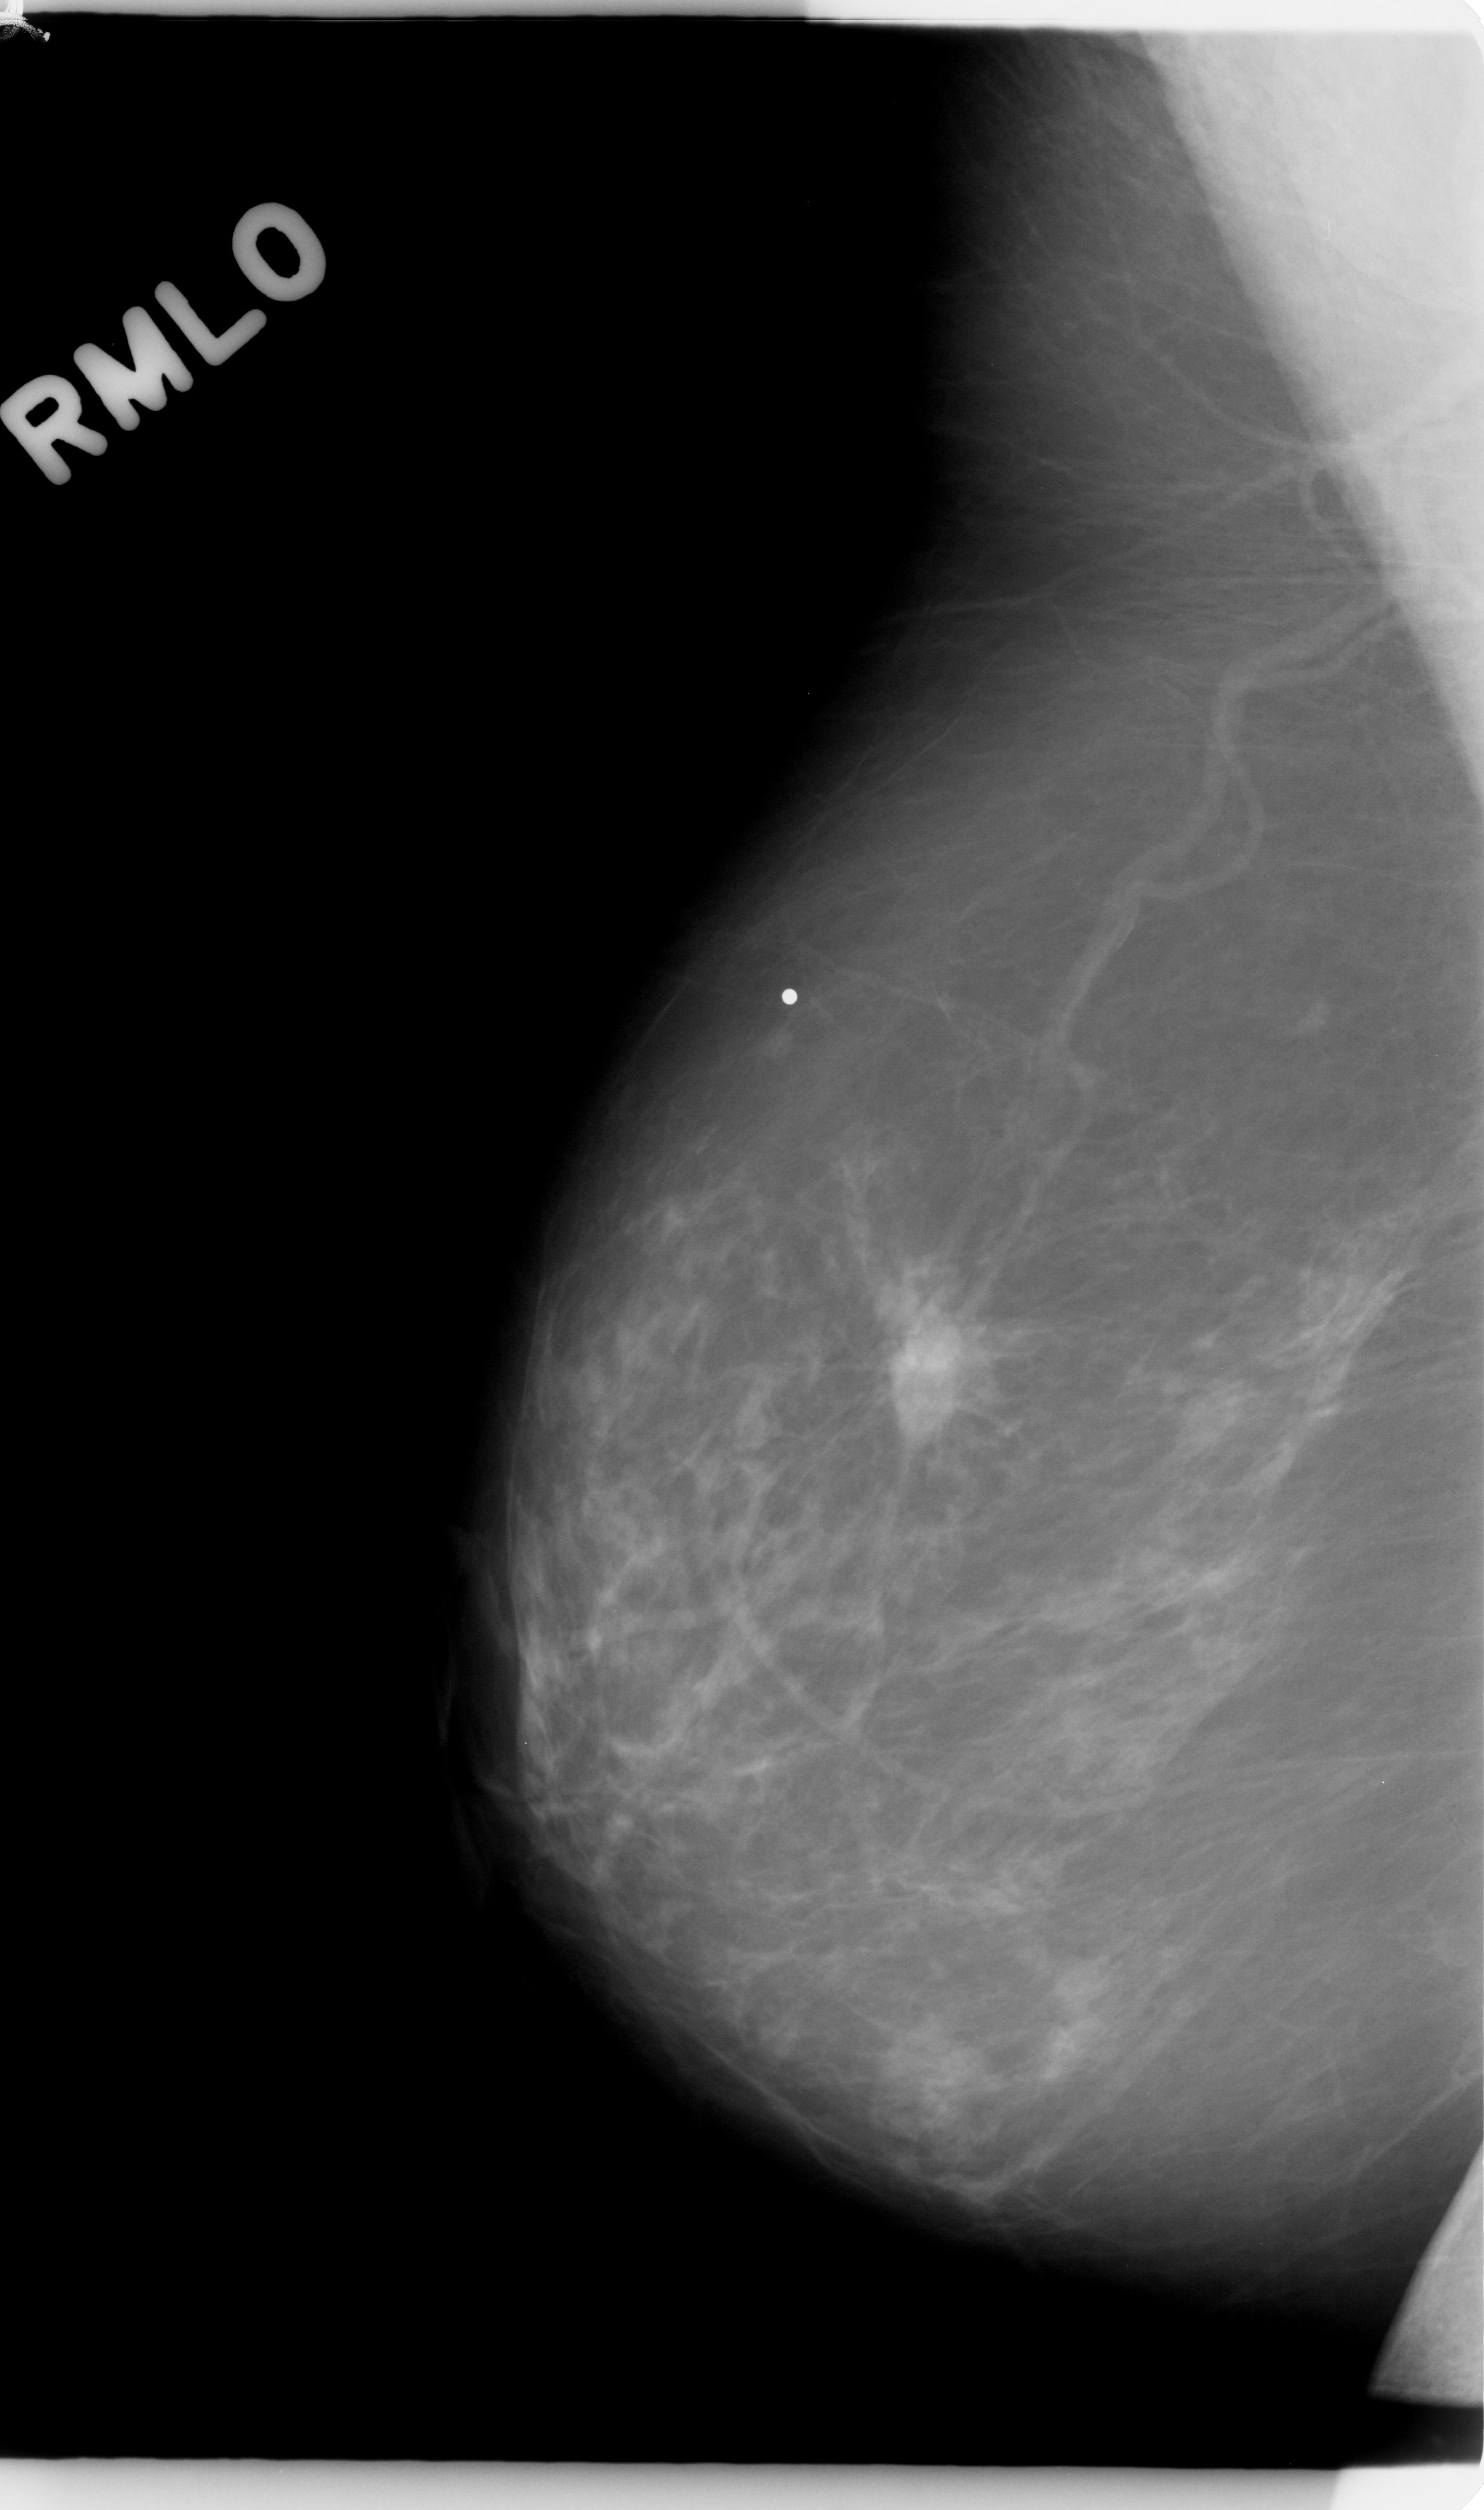
Digitized screen-film mammogram; right breast; mediolateral oblique (MLO) view; BI-RADS breast density category 1 (scale 1–4).
Finding: mass, shape irregular, margins spiculated; BI-RADS assessment category 5; subtlety rating 5 on a 1 (subtle) to 5 (obvious) scale; pathology (as recorded): malignant.